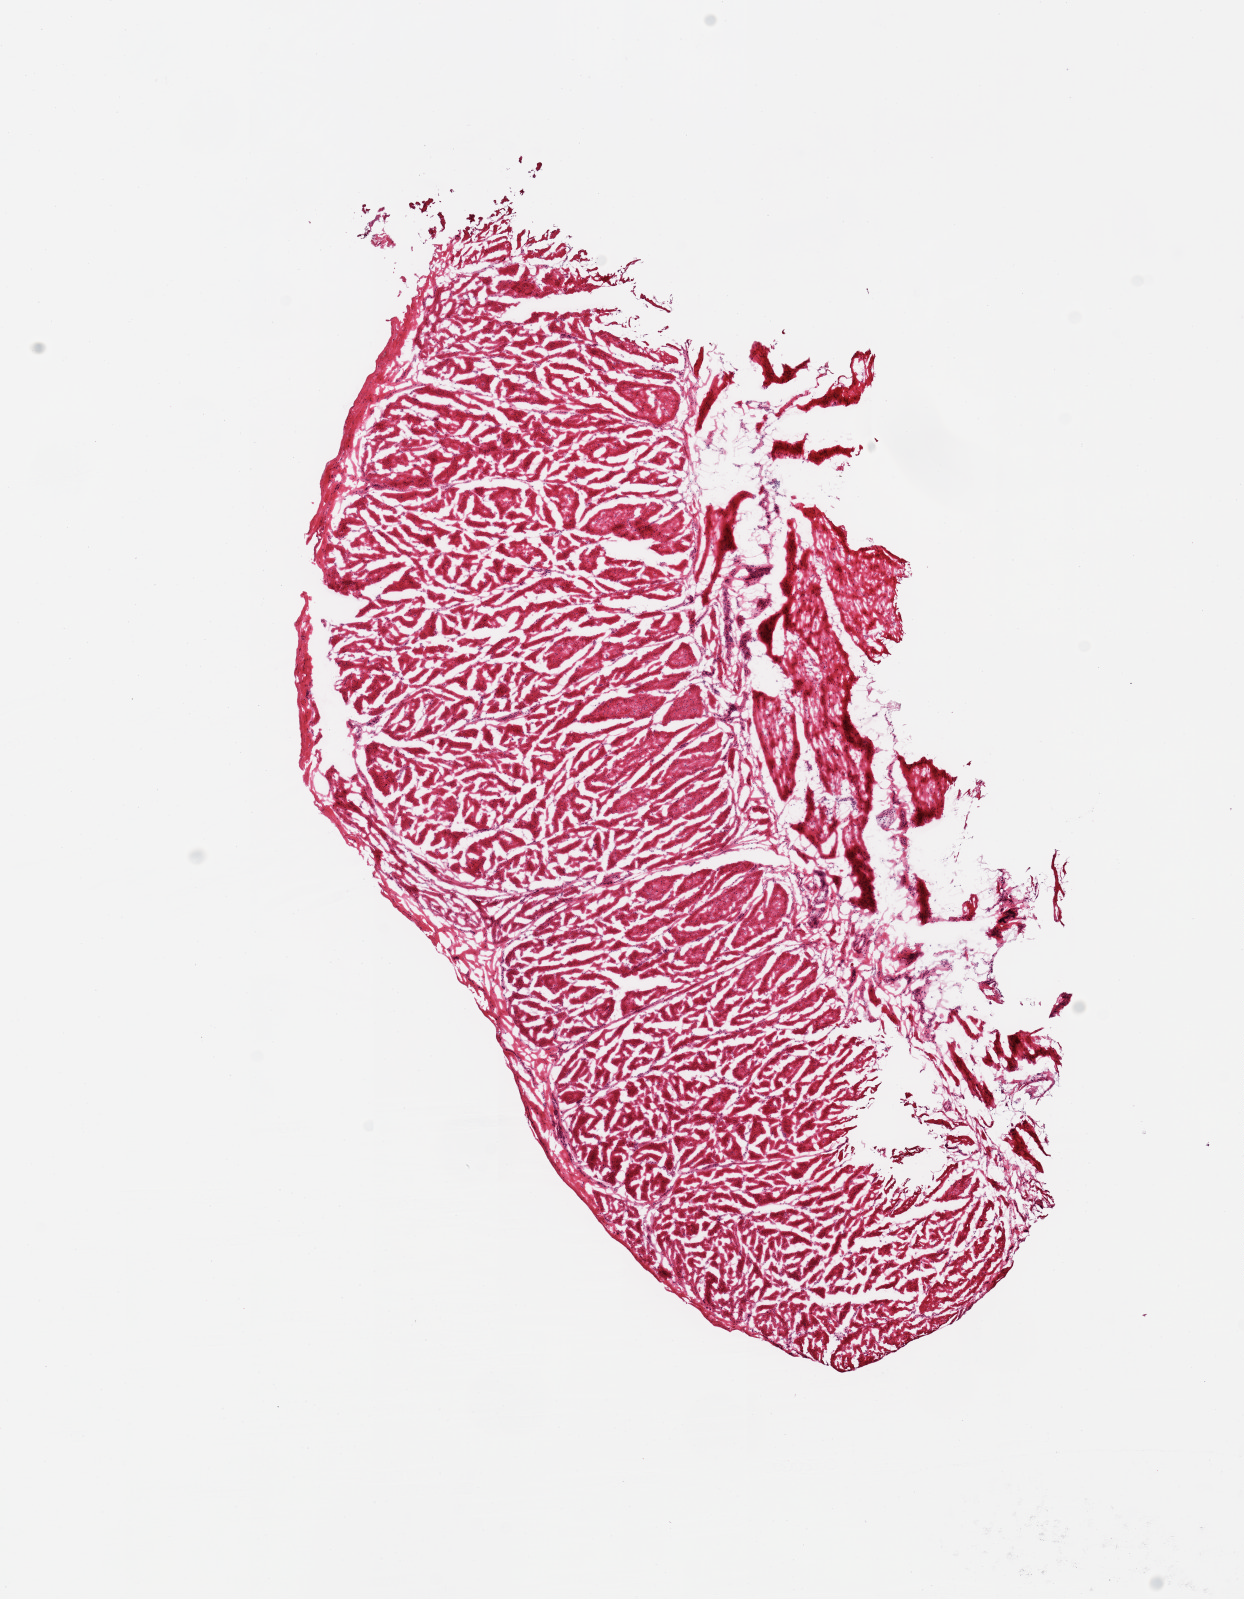
Digitized H&E-stained section, brightfield — a low-resolution overview of the entire scanned area, about 9.8 x 12.7 mm. Donor sex: female.
- specimen: frozen section (dry ice); target tissue: esophageal muscle; tissue donor sample